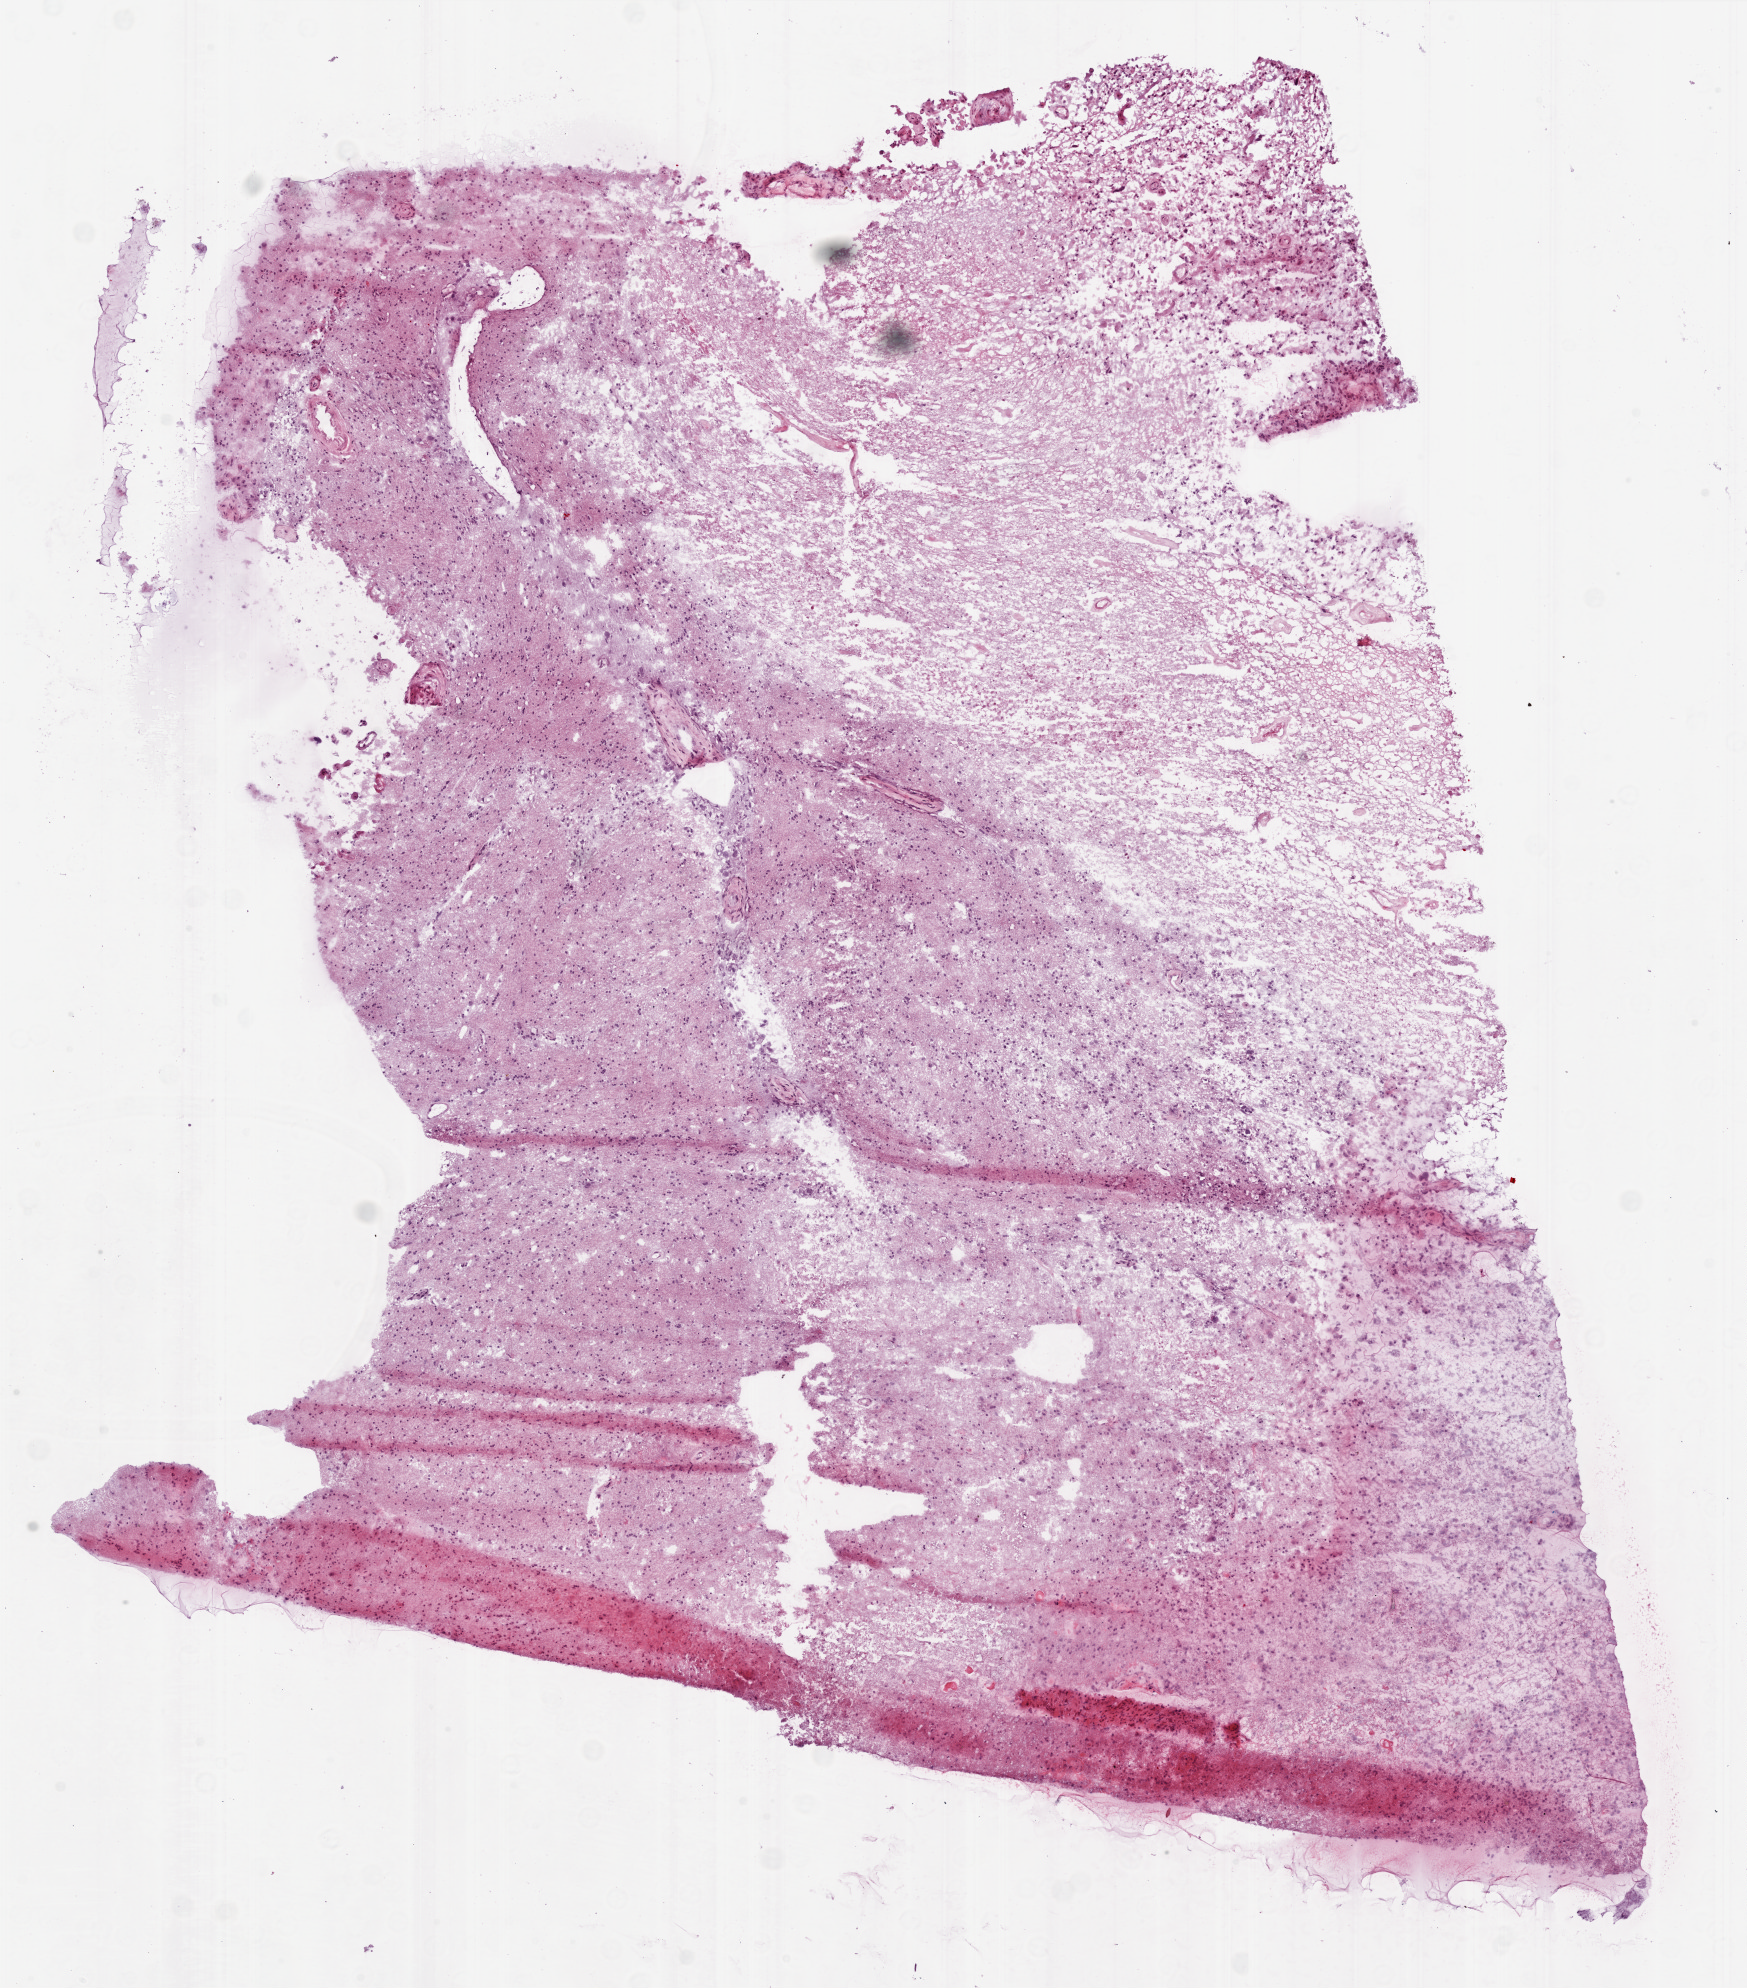
Digitized H&E-stained tissue section (whole slide), shown as a low-resolution overview of the whole scanned area (about 7.0 x 8.0 mm). Slide review estimates, as recorded: tumour cells 1%, tumour nuclei 50%, normal cells 0%, stromal cells 40%, necrosis 60%. Inflammatory infiltration, as recorded: lymphocyte infiltration 0%, monocyte infiltration 90%, neutrophil infiltration 0%.
Specimen: frozen section from the bottom of the tissue portion; sample: primary tumour, brain.